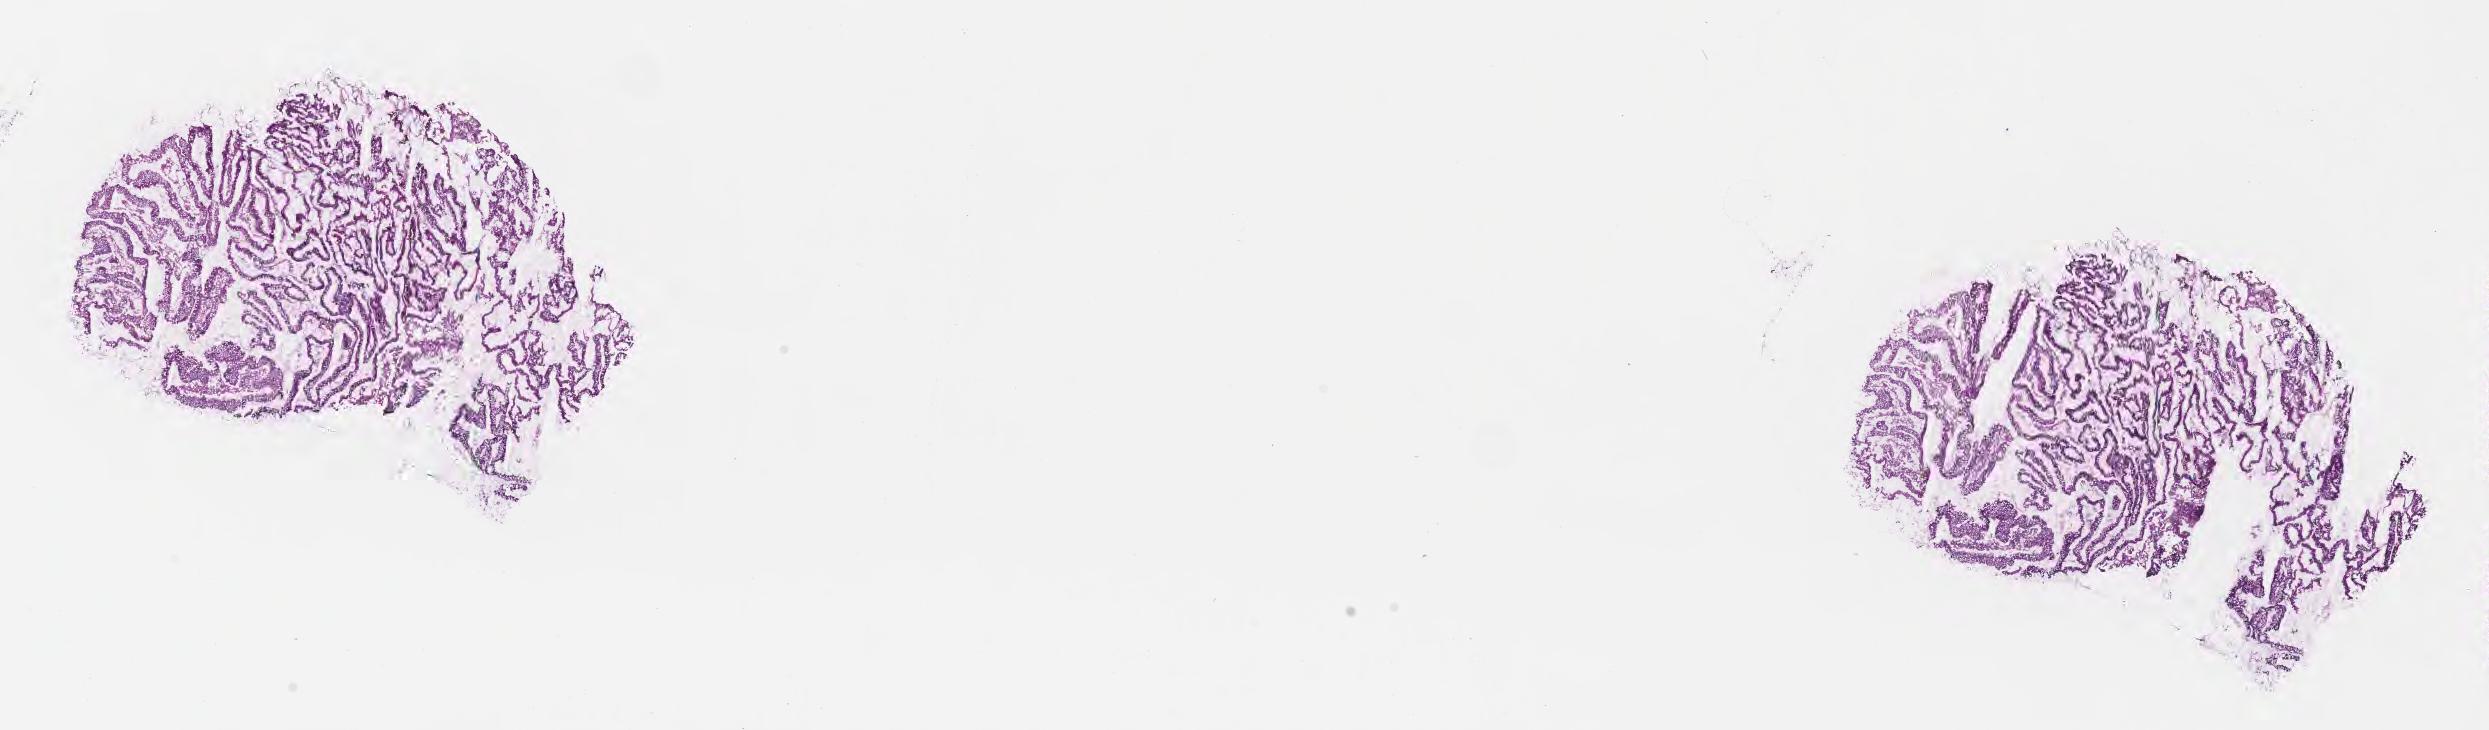
Whole-slide image, H&E stain — shown as a low-resolution overview of the whole scanned area (about 20.1 x 5.9 mm), frozen section, premalignant lesion from a patient with tubulovillous adenoma, NOS, anatomic site: cecum. Patient: female, age at initial diagnosis 62 years. Composition of this section per pathologist review: tumor cells 88%, tumor nuclei 88%, stromal cells 12%, necrosis 0%, normal cells 0%. Infiltration values recorded for this section: lymphocyte infiltration 9%, monocyte infiltration 1%, neutrophil infiltration 0%.
This section: sample classed premalignant; the patient's recorded diagnosis is given above. Section: bottom of the tissue portion.